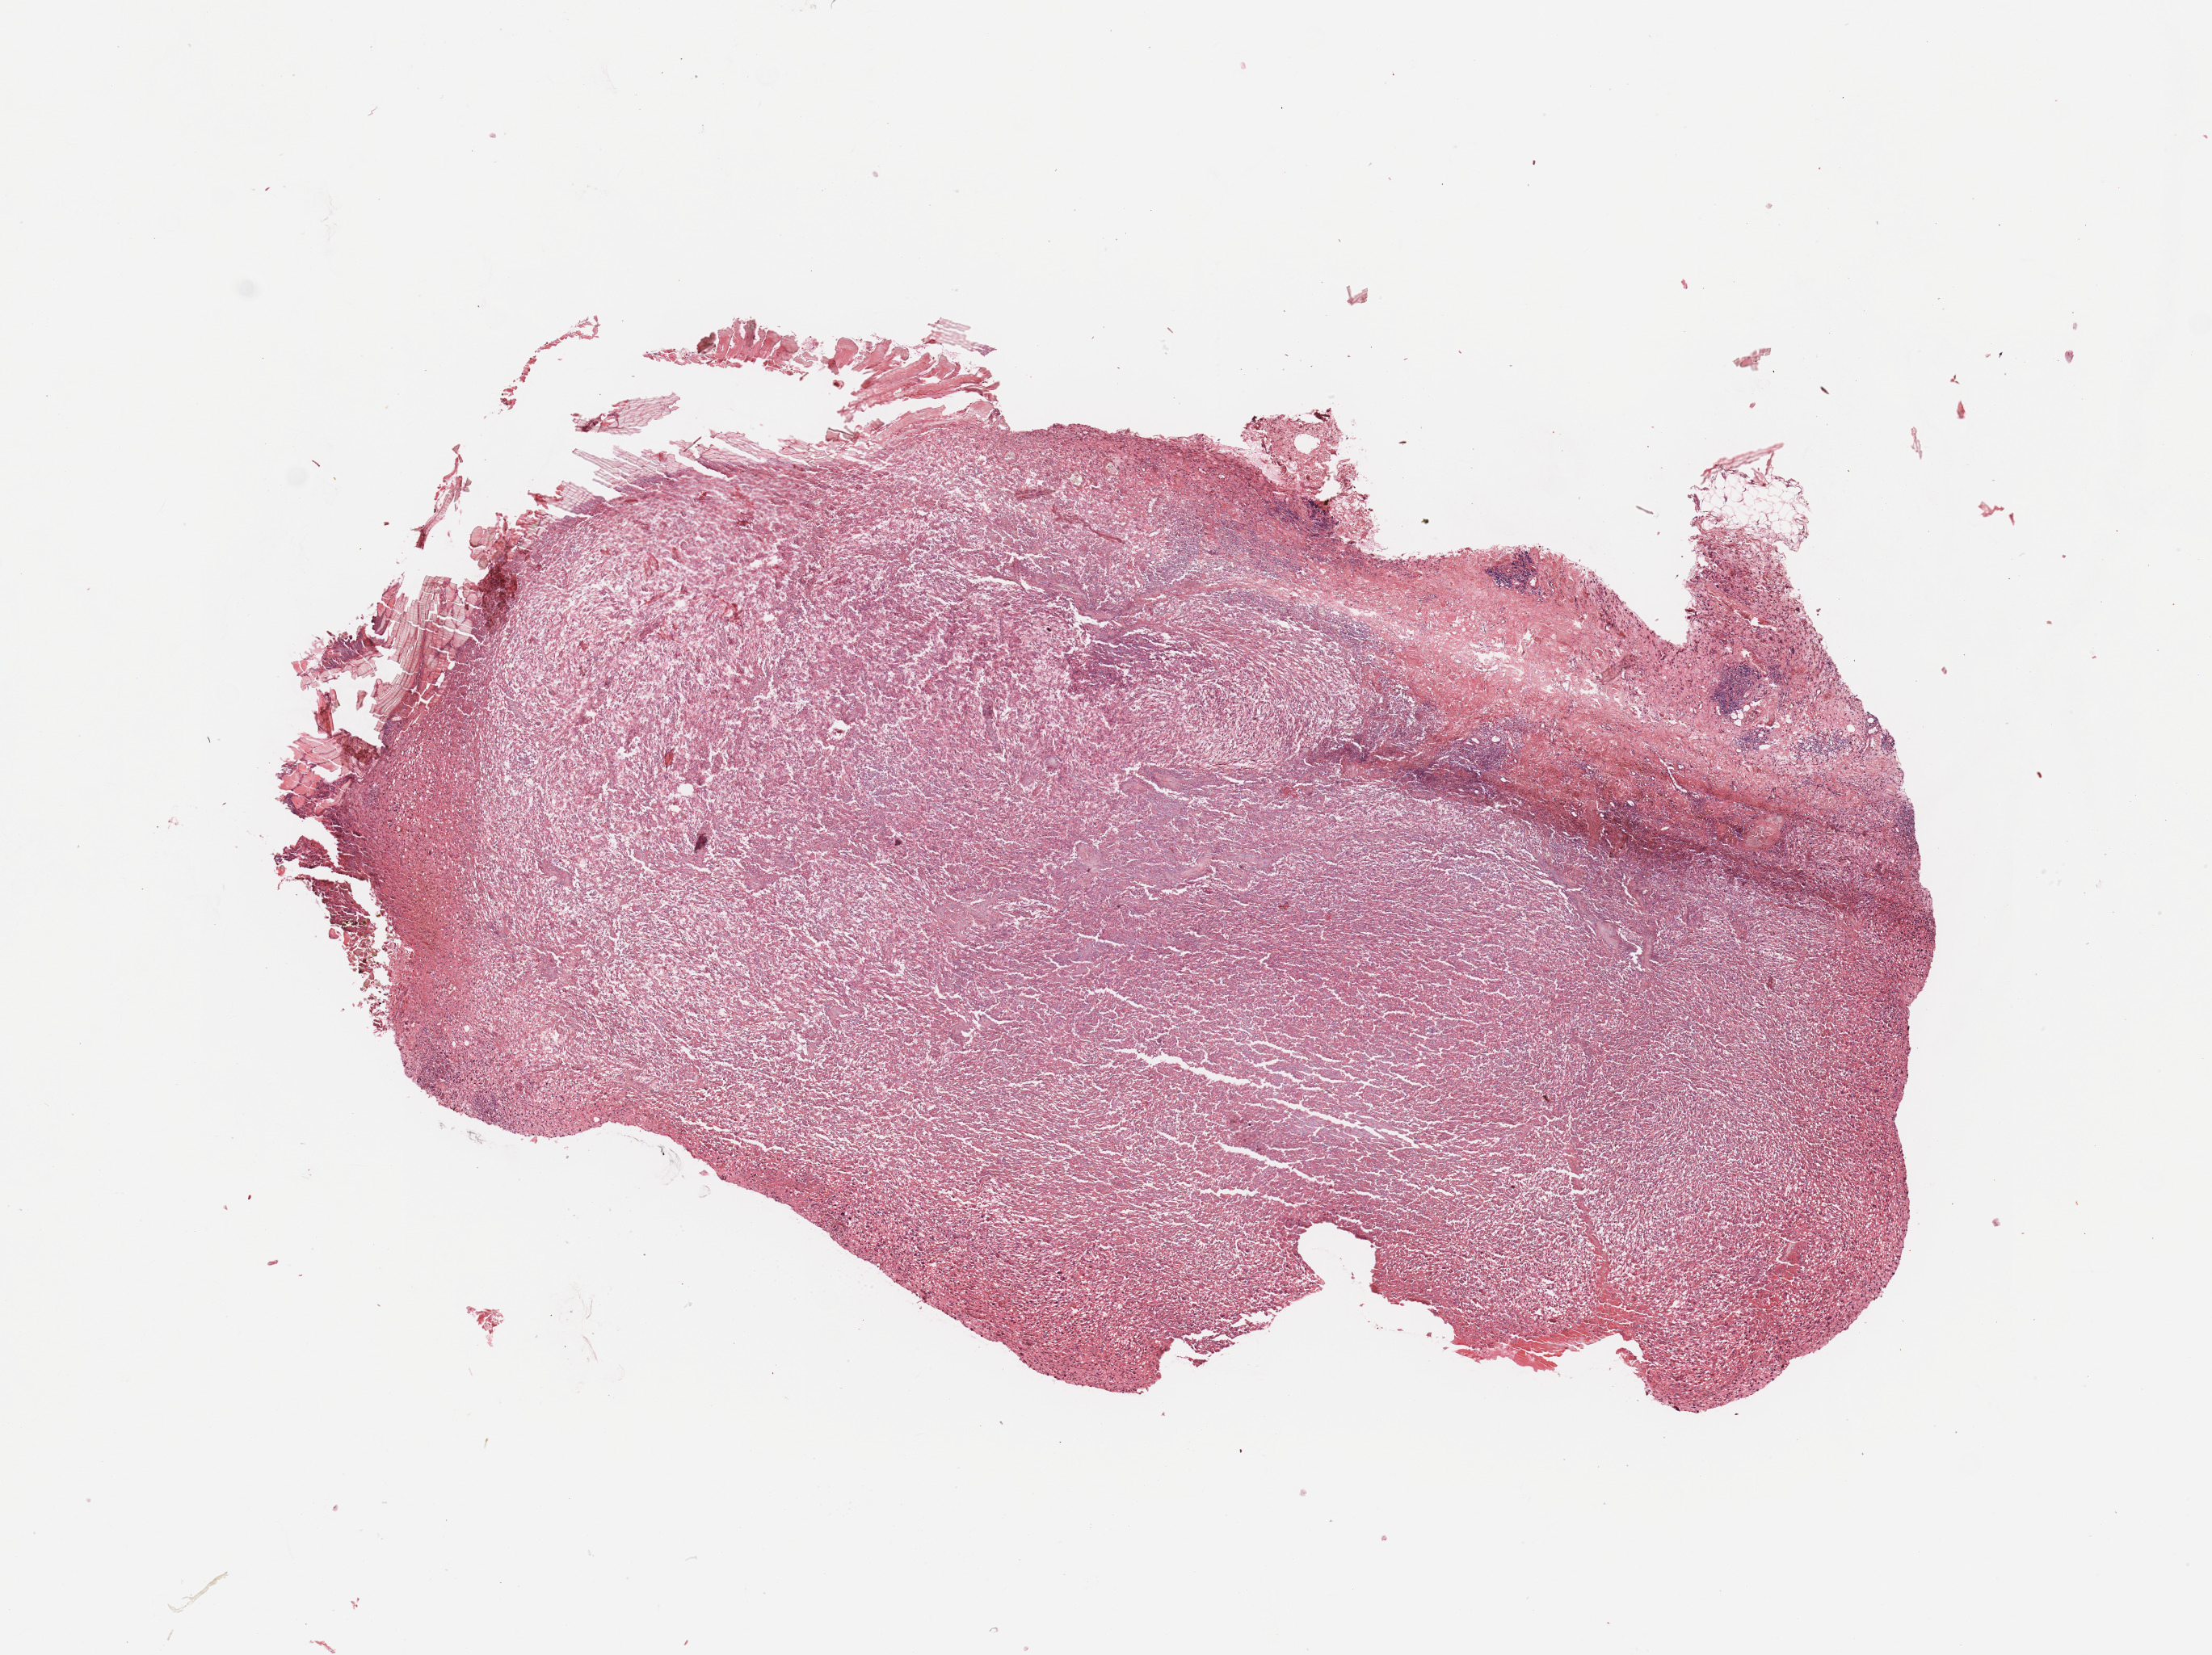
Digitized H&E tissue section (whole slide), shown as a low-resolution overview of the whole scanned area (about 10.8 x 8.1 mm, slide scanned at 20x); tumour tissue sample. Male, 53 y/o.
Patient diagnosis (cohort enrolment): sarcoma (site not recorded at cohort level). Primary tumour site (as recorded): chest.